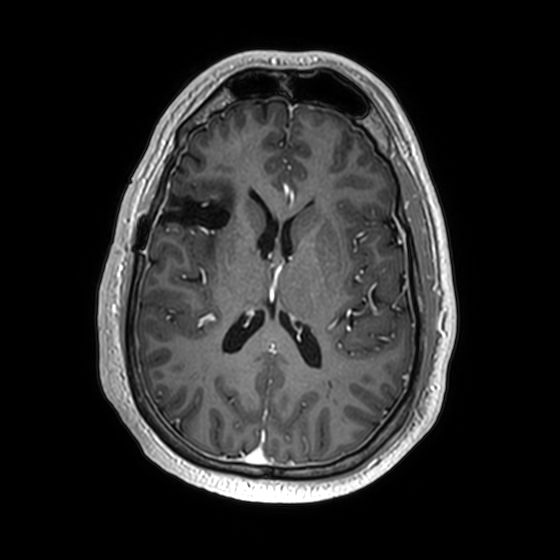
Brain MRI from a brain-tumour surgery series, one axial slice; slice 80 of 174 in the series (ordered by position); T1-weighted post-contrast; 1 mm slice thickness; 560 × 560 image matrix, field of view 256 × 256 mm. Case-level facts recorded for this patient, not image findings: histopathology: Astrocytoma; WHO grade: 2; IDH mutation: yes.
Structures marked on this image (outlined manually by an expert reader):
- previous resection cavity: bounding box [x1, y1, x2, y2] px = [158, 196, 230, 229]